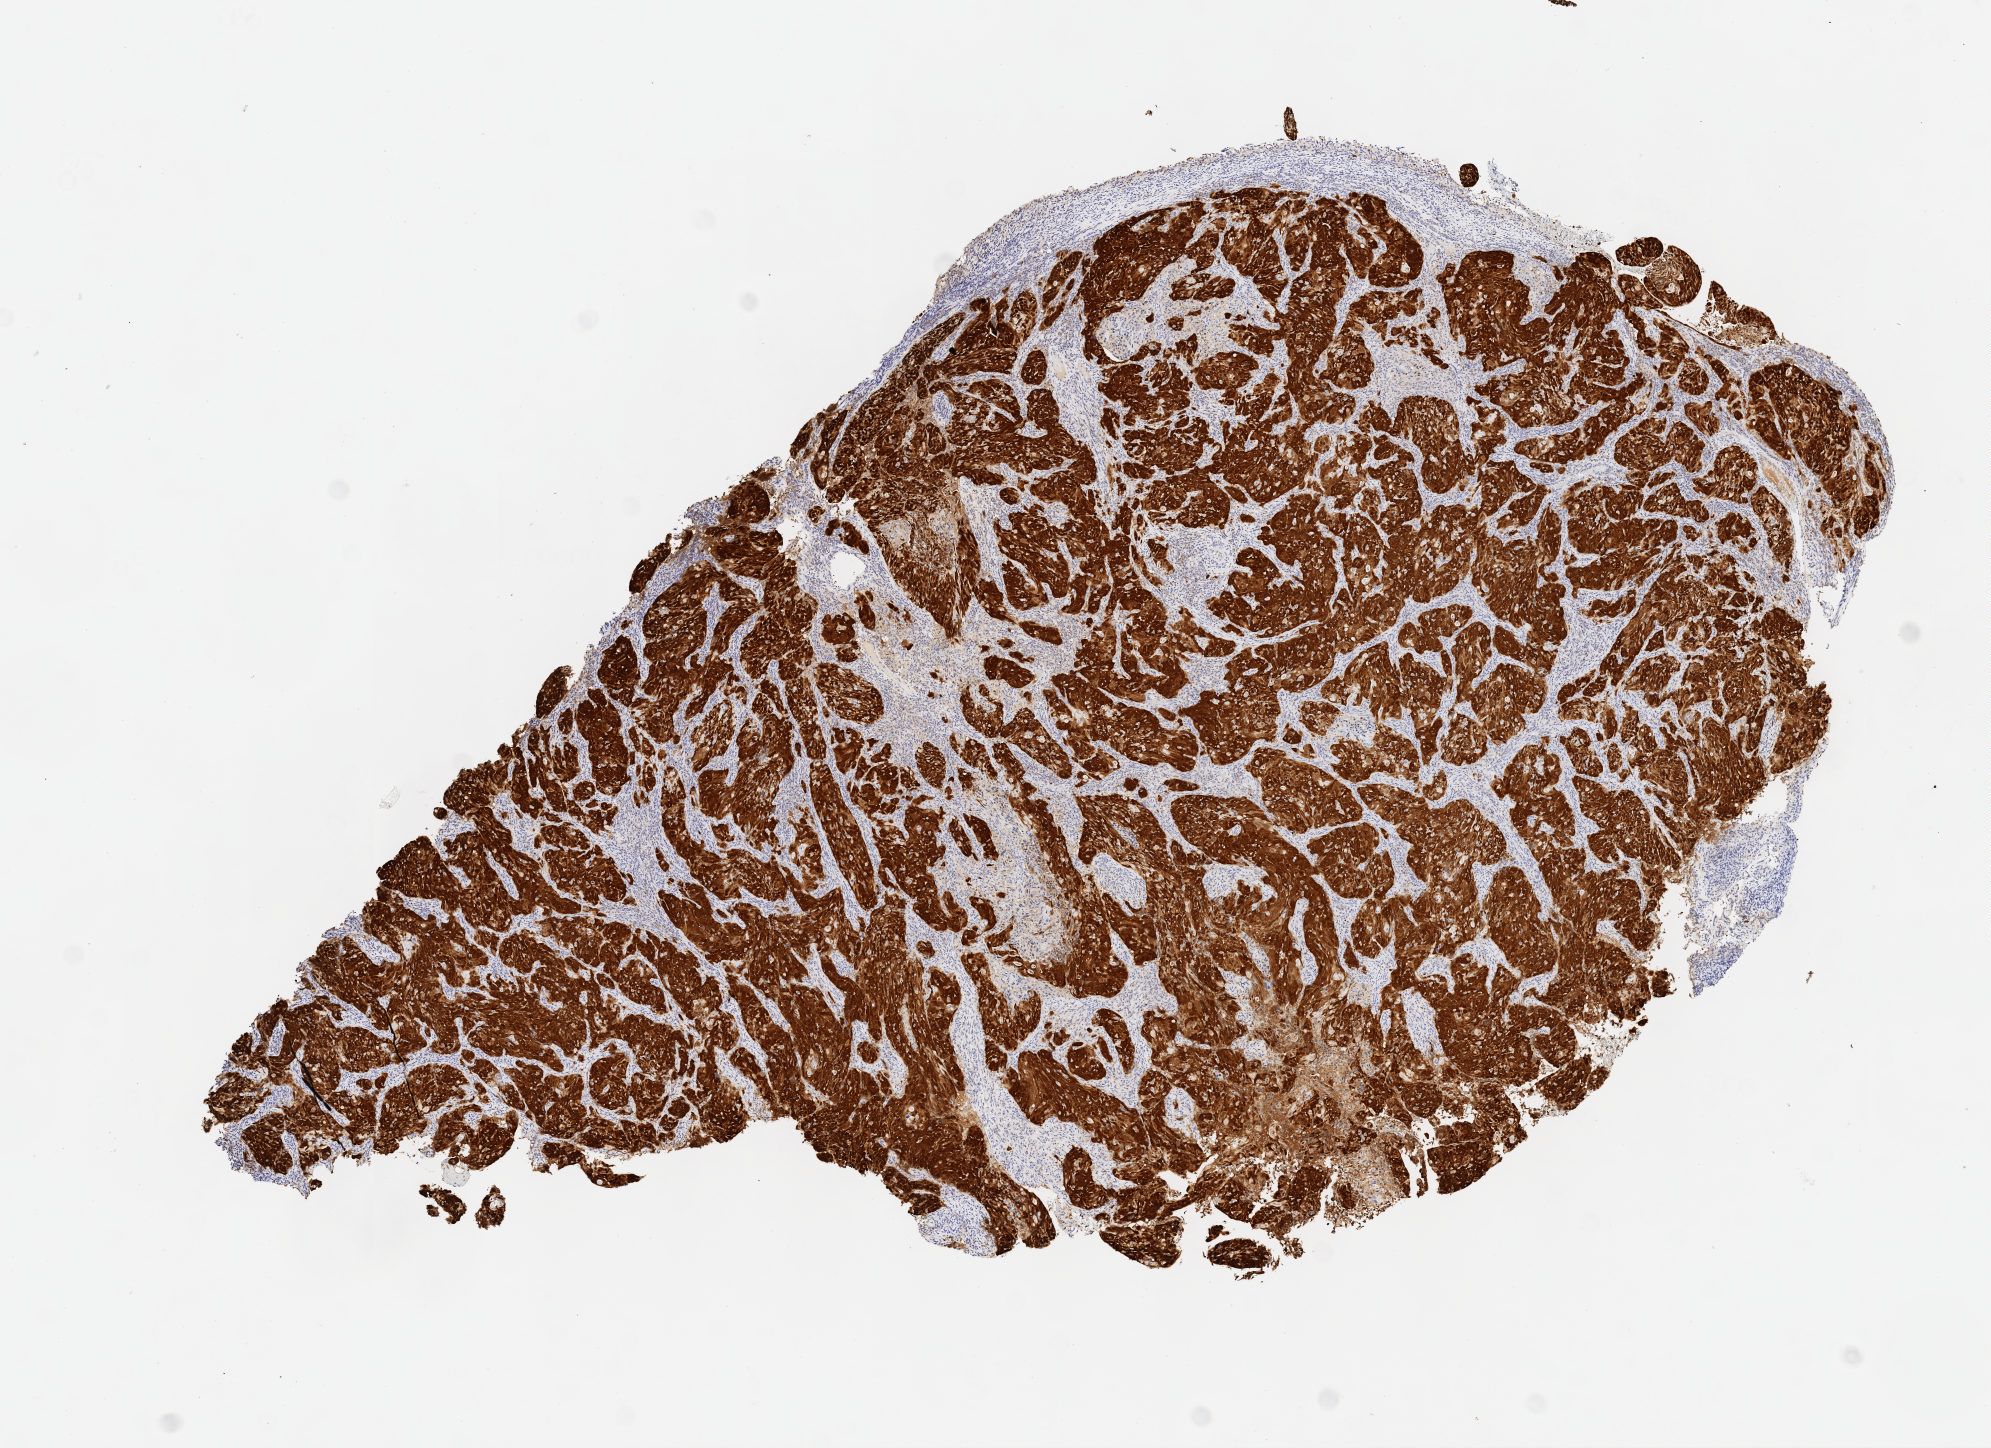
Immunohistochemistry (IHC) whole-slide image stained for p16 (p16INK4a) — low-resolution overview of the scanned area, about 8.1 x 5.9 mm, tumor tissue, anatomic site: cervix. Female patient, aged 68.
Histologic diagnosis: Squamous cell carcinoma, large cell, nonkeratinizing, NOS.